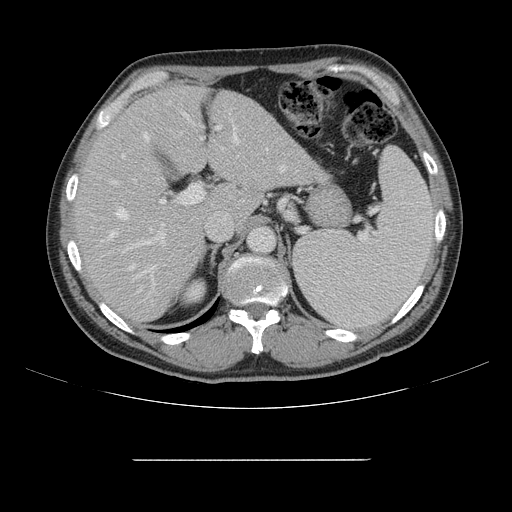
Contrast-enhanced abdominal CT, one axial slice; position 101 of 164 along the scan axis; 120 kVp; intravenous contrast given; soft-tissue window (W 400 / L 40 HU); 2.5 mm slice thickness; 512 × 512 image matrix, field of view 404 × 404 mm. Male patient, age 54 years. Case-level facts recorded for this patient, not image findings: diagnosis: colorectal cancer liver metastases, imaged before liver resection; multiple liver metastases: yes; largest metastasis: 1 cm; chemotherapy before resection: yes.
Annotated regions visible in this slice (expert manual segmentation):
- hepatic veins: bounding box [x1, y1, x2, y2] px = [108, 130, 285, 270]
- liver: [77, 86, 323, 323]
- planned liver remnant (the part of the liver to remain after resection): [77, 86, 237, 323]
- portal vein (with intrahepatic branches): [120, 102, 238, 306]